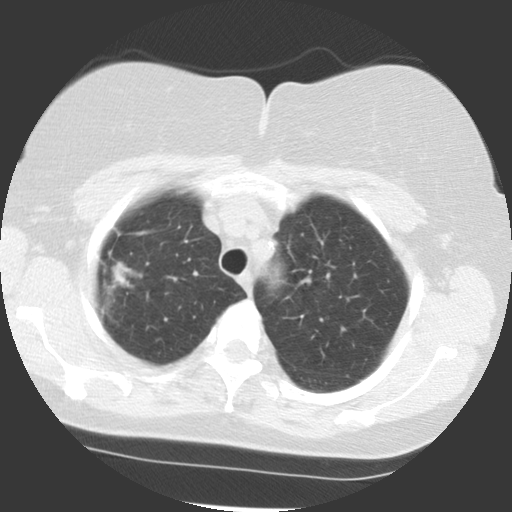
Low-dose screening chest CT, one axial slice; slice 93 of 113 in the series (ordered by position); reconstruction kernel STANDARD; 140 kVp; lung window (W 1500 / L -600 HU); 512 × 512 image matrix, field of view 320 × 320 mm.
Outlined on this slice (expert manual segmentation):
- lesion 1 (tumor, upper lobe of right lung): bounding box <112,262,135,287> (left, top, right, bottom; pixels)